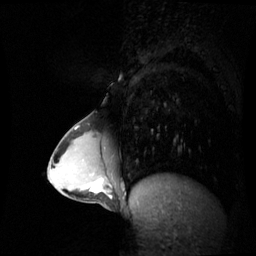
Breast MRI (dynamic contrast-enhanced), one sagittal slice. Slice 24 of 60 in the series (ordered by position). Dynamic contrast-enhanced series, image 2 of 3 at this slice position (ordered by acquisition). 1.5 T. TE 4.2 ms, TR 8.9 ms. 2.4 mm slice thickness. 256 × 256 image matrix, field of view 300 × 300 mm. Patient: female, 34 years. From the clinical record (not read from this slice): setting: breast cancer imaged before/during neoadjuvant chemotherapy; receptor status: triple-negative.
Annotated regions visible in this slice (semi-automatic segmentation, software-assisted and operator-edited):
- analysis volume of interest (the breast-tissue region the enhancement analysis was run in; not a lesion): bounding box <65,168,112,204> (left, top, right, bottom; pixels)
- tumour enhancement mask (voxels above the 70 % enhancement threshold inside the analysis volume of interest): <90,178,103,193>